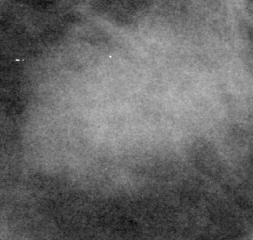
Cropped region of a digitized screen-film mammogram centred on a radiologist-marked abnormality, left breast, CC view.
- Mass, shape oval, margins microlobulated; BI-RADS assessment category 4; subtlety rating 5 on a 1 (subtle) to 5 (obvious) scale; pathology result (as recorded, not read from the image): malignant.